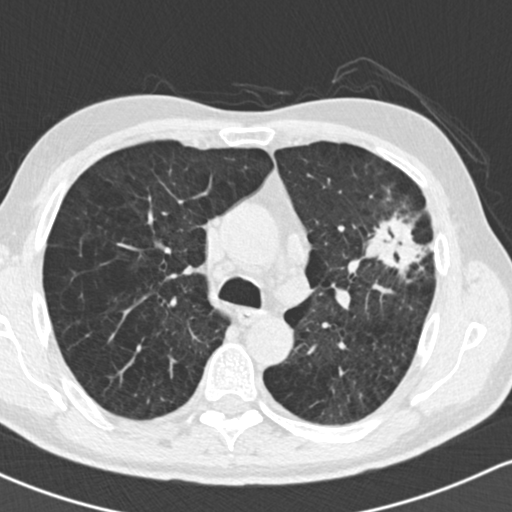
Axial slice from a low-dose chest CT screening exam; baseline annual screen; lung window (W 1500 / L -600 HU); 2 mm slice thickness; standard (soft-tissue) reconstruction kernel (B30f); slice 59 of 162 in the series; 512 × 512 image matrix, field of view 318 × 318 mm. Male, age 61 years at enrolment. Former smoker at enrolment.
Expert reader's lesion annotation, bounding box <355,185,452,292> (left, top, right, bottom; pixels). Screening reader's record for this exam (one nodule recorded; not confirmed to be the boxed lesion): non-calcified nodule or mass ≥4 mm, left upper lobe, 35 × 35 mm, spiculated (stellate) margins, soft tissue attenuation. Lung cancer was diagnosed 19 days after this screen: adenocarcinoma, NOS, left upper lobe, well differentiated (G1), stage IIIA (AJCC 6th edition), 45 mm at pathology.